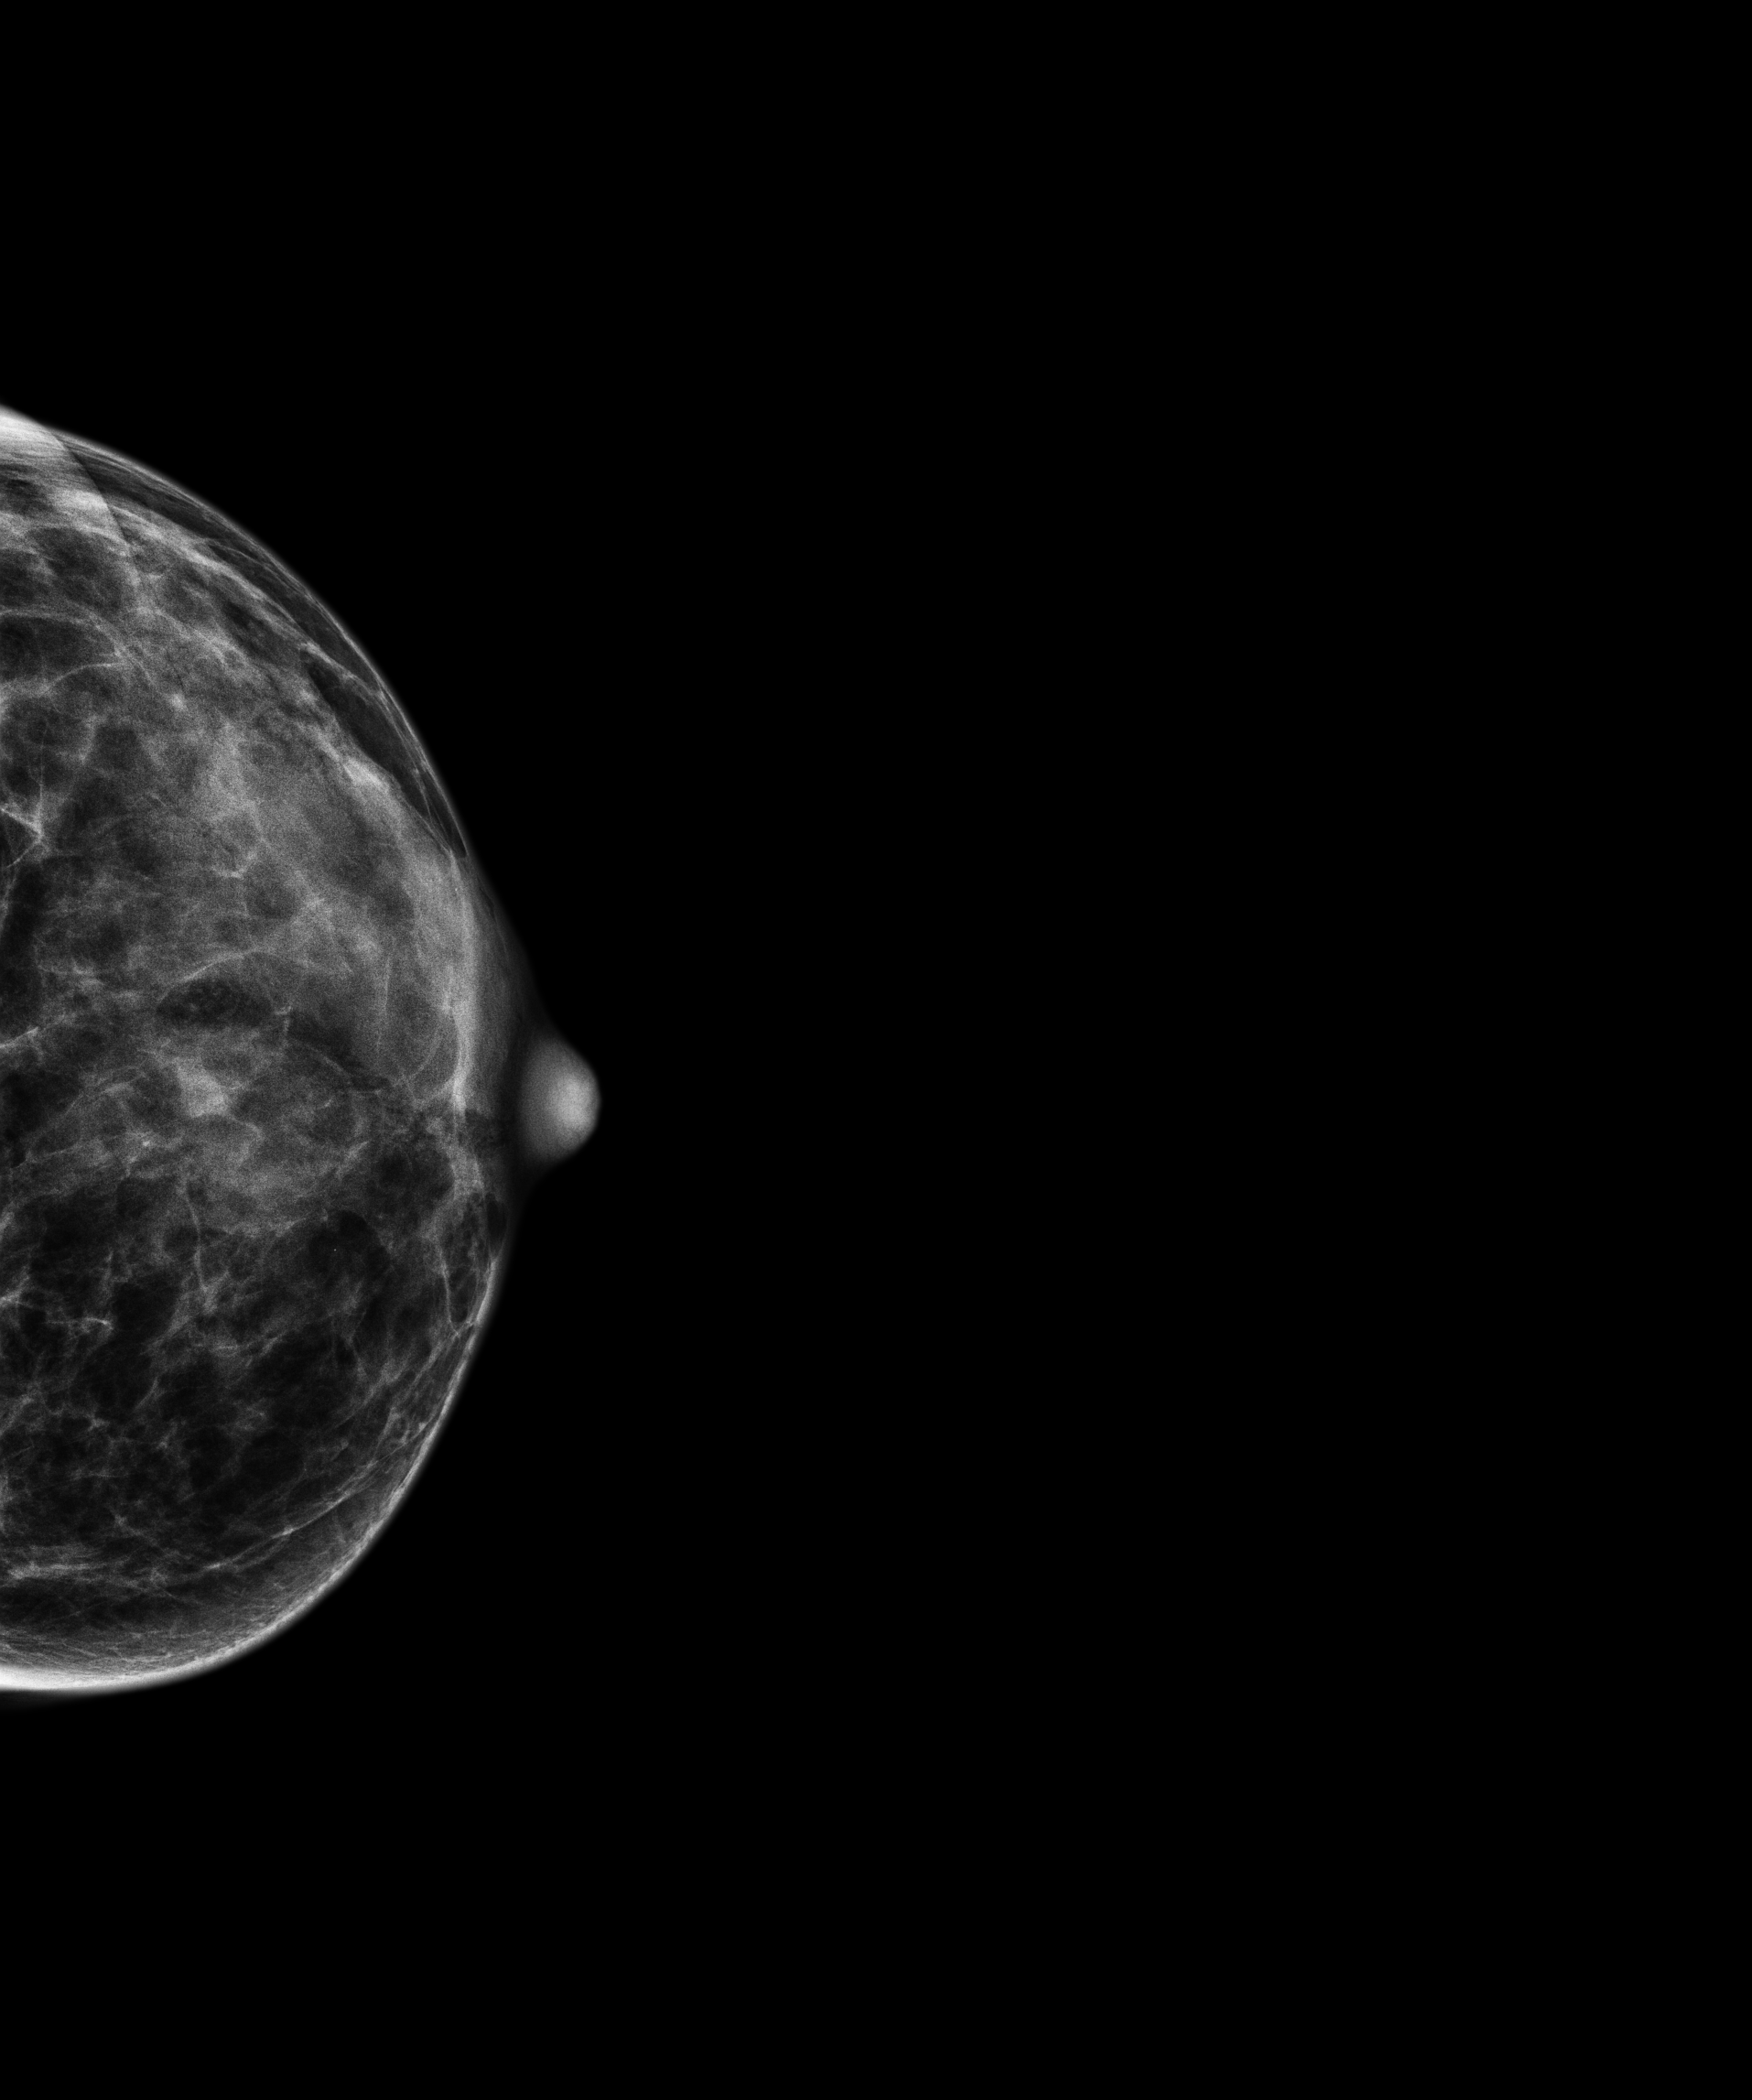
Annual screening mammography examination, system: Senographe Pristina. Female patient, age 55 years.
Image type: full-field digital mammogram. Breast: left. Projection: craniocaudal (CC) view.